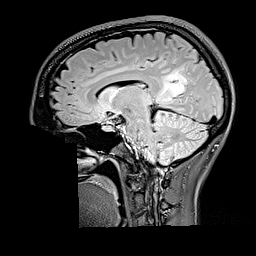
Brain MRI from a brain-tumour surgery series, one sagittal slice. Slice 95 of 176 in the series (ordered by position). T2 FLAIR. 1 mm slice thickness. 256 × 256 image matrix. Case-level facts recorded for this patient, not image findings: histopathology: Oligodendroglioma; WHO grade: 2; IDH mutation: yes.
Structures marked on this image (manually delineated by an expert):
- tumour: bounding box <160,67,188,104> (left, top, right, bottom; pixels)